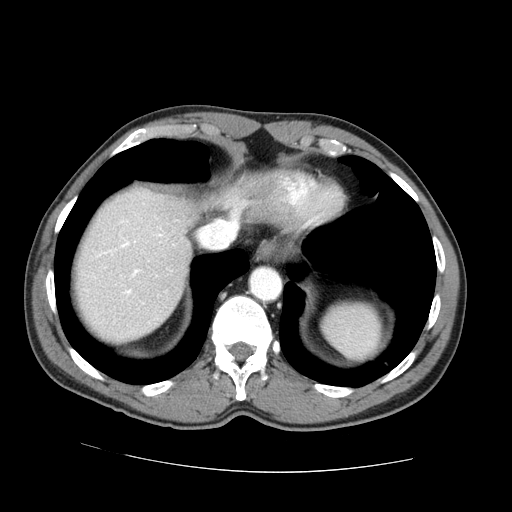
Contrast-enhanced abdominal CT (liver protocol), one axial slice; slice 62 of 73 in the series (ordered by position); reconstruction kernel STANDARD; 100 kVp; one of 2 acquisitions stored at this slice position; soft-tissue window (W 400 / L 40 HU); 2.5 mm slice thickness; 512 × 512 image matrix, field of view 380 × 380 mm. From the clinical record (not read from this slice): diagnosis: hepatocellular carcinoma (patient treated with transarterial chemoembolisation; whether this scan precedes or follows treatment is not stated here); TNM stage (as recorded): Stage-IVA; Child-Pugh class: A.
Annotated regions visible in this slice (semi-automatically segmented with operator editing):
- abdominal aorta: box from (x=252, y=268) to (x=280, y=301) px
- liver parenchyma outside the tumour (the mass and vessels are separate outlines, so this box may not span the whole liver): (x=76, y=188)–(x=198, y=342)
- liver vessels: (x=121, y=242)–(x=139, y=294)